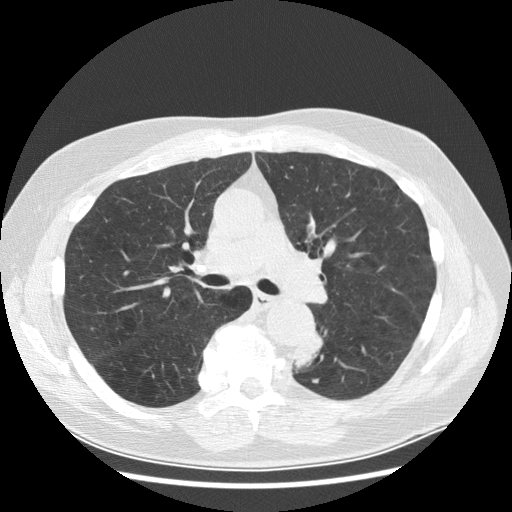
Low-dose screening chest CT, axial slice; baseline screening round; lung window (W 1500 / L -600 HU); 2.5 mm slice thickness; 512 × 512 image matrix, field of view 370 × 370 mm. Male, age 70 years at enrolment.
Expert reader's lesion annotation, bounding box [x1, y1, x2, y2] px = [278, 328, 330, 384]. Screening reader's record for this exam (one nodule recorded; not confirmed to be the boxed lesion): non-calcified nodule or mass ≥4 mm, left lower lobe, 27 × 16 mm, spiculated (stellate) margins, soft tissue attenuation, pre-existing on the prior screen: yes; interval growth: yes. Official screen result: positive, change unspecified: nodule(s) >= 4 mm or enlarging nodule(s), mass(es), or other non-specific abnormalities suspicious for lung cancer. Participant outcome: lung cancer diagnosed 97 days after this screen — papillary adenocarcinoma, NOS, left lower lobe, moderately differentiated (G2), stage IB (AJCC 6th edition), 35 mm at pathology.